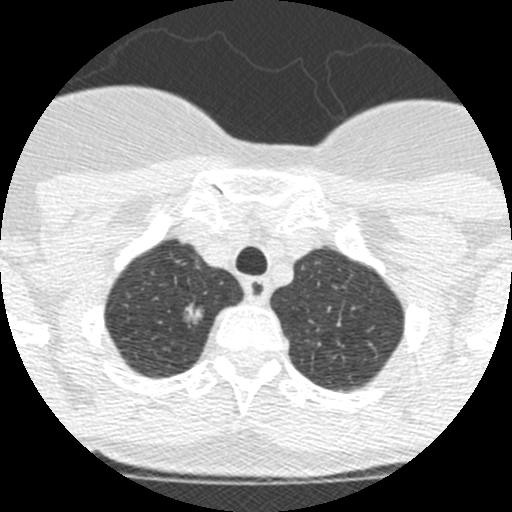
Low-dose screening chest CT, one axial slice; slice 213 of 250 in the series (ordered by position); reconstruction kernel STANDARD; lung window (W 1500 / L -600 HU); 512 × 512 image matrix, field of view 257 × 257 mm.
Outlined on this slice (expert manual segmentation):
- lesion 1 (tumor, upper lobe of right lung): bounding box (x1, y1, x2, y2) in pixels: (185, 304, 203, 324)